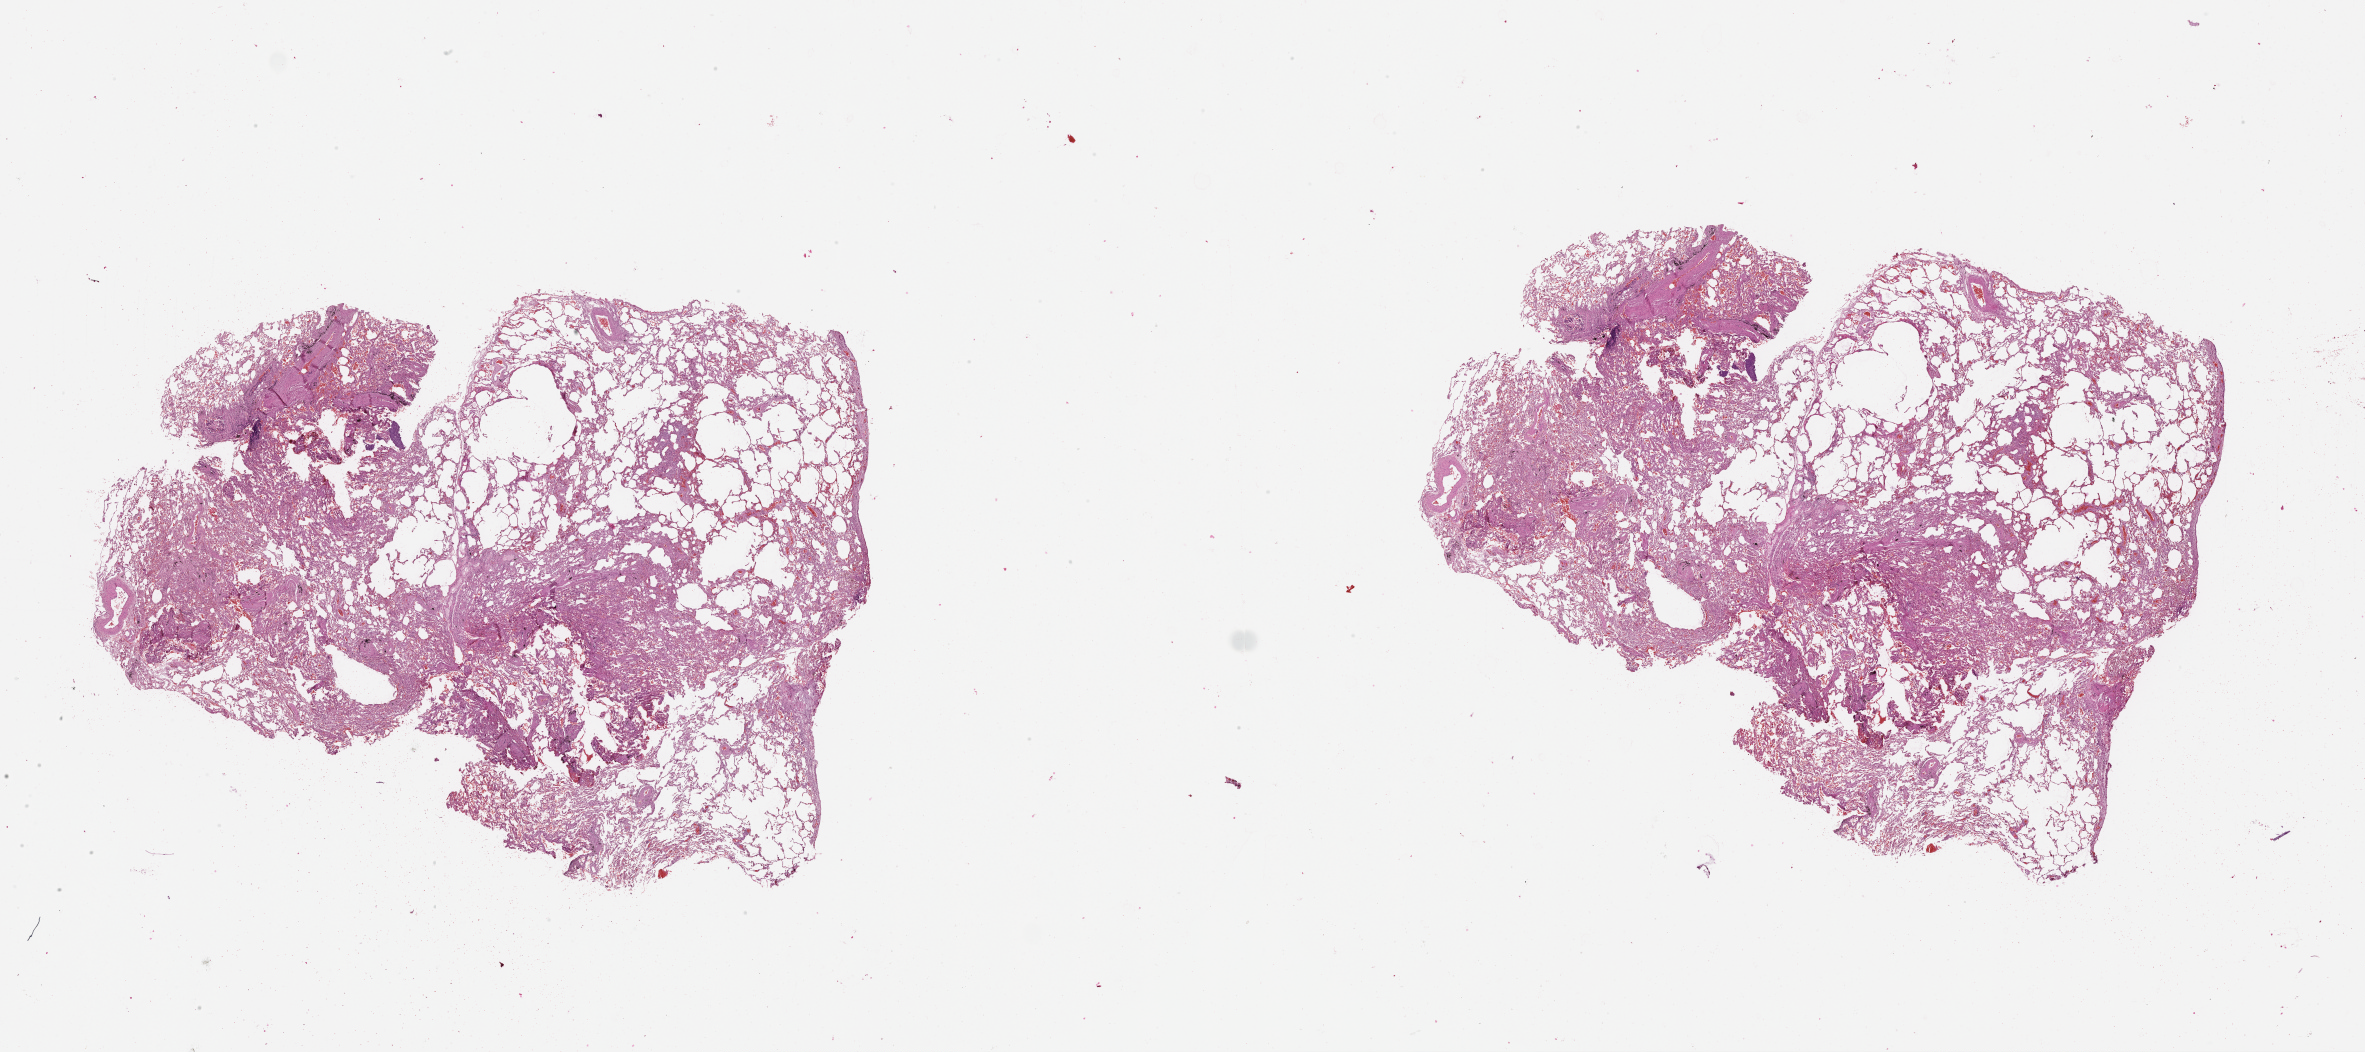
H&E whole-slide image, a low-resolution overview of the entire scanned area, about 38.1 x 16.9 mm (slide scanned at 20x). Lung, normal (non-tumour) tissue. 59-year-old male patient.
• this section: normal (non-tumour) tissue from the same patient
• patient diagnosis (cohort enrolment): squamous cell carcinoma (lung)